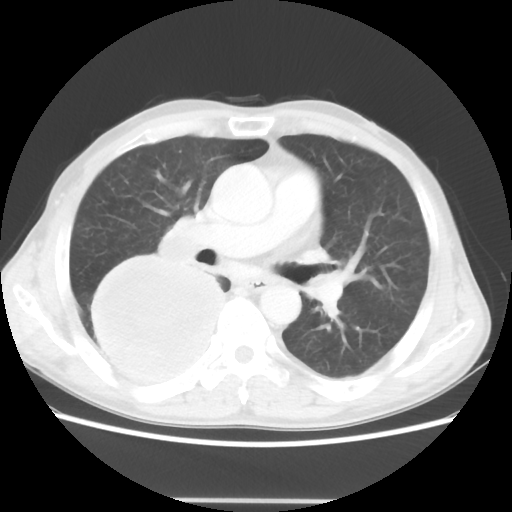
Chest CT, one axial slice; slice 27 of 48 in the series (ordered by position); reconstruction kernel STANDARD; 100 kVp; lung window (W 1500 / L -600 HU); 5 mm slice thickness; 512 × 512 image matrix, field of view 361 × 361 mm. Male patient, age 66 years. From the clinical record (not read from this slice): clinical TNM (as recorded): T4 N1 M1; histopathological grade: G3.
Structures marked on this image (rectangle marked by the reading radiologist):
- lung tumour (recorded histology: small cell carcinoma): bounding box (x1, y1, x2, y2) in pixels: (84, 254, 231, 397)